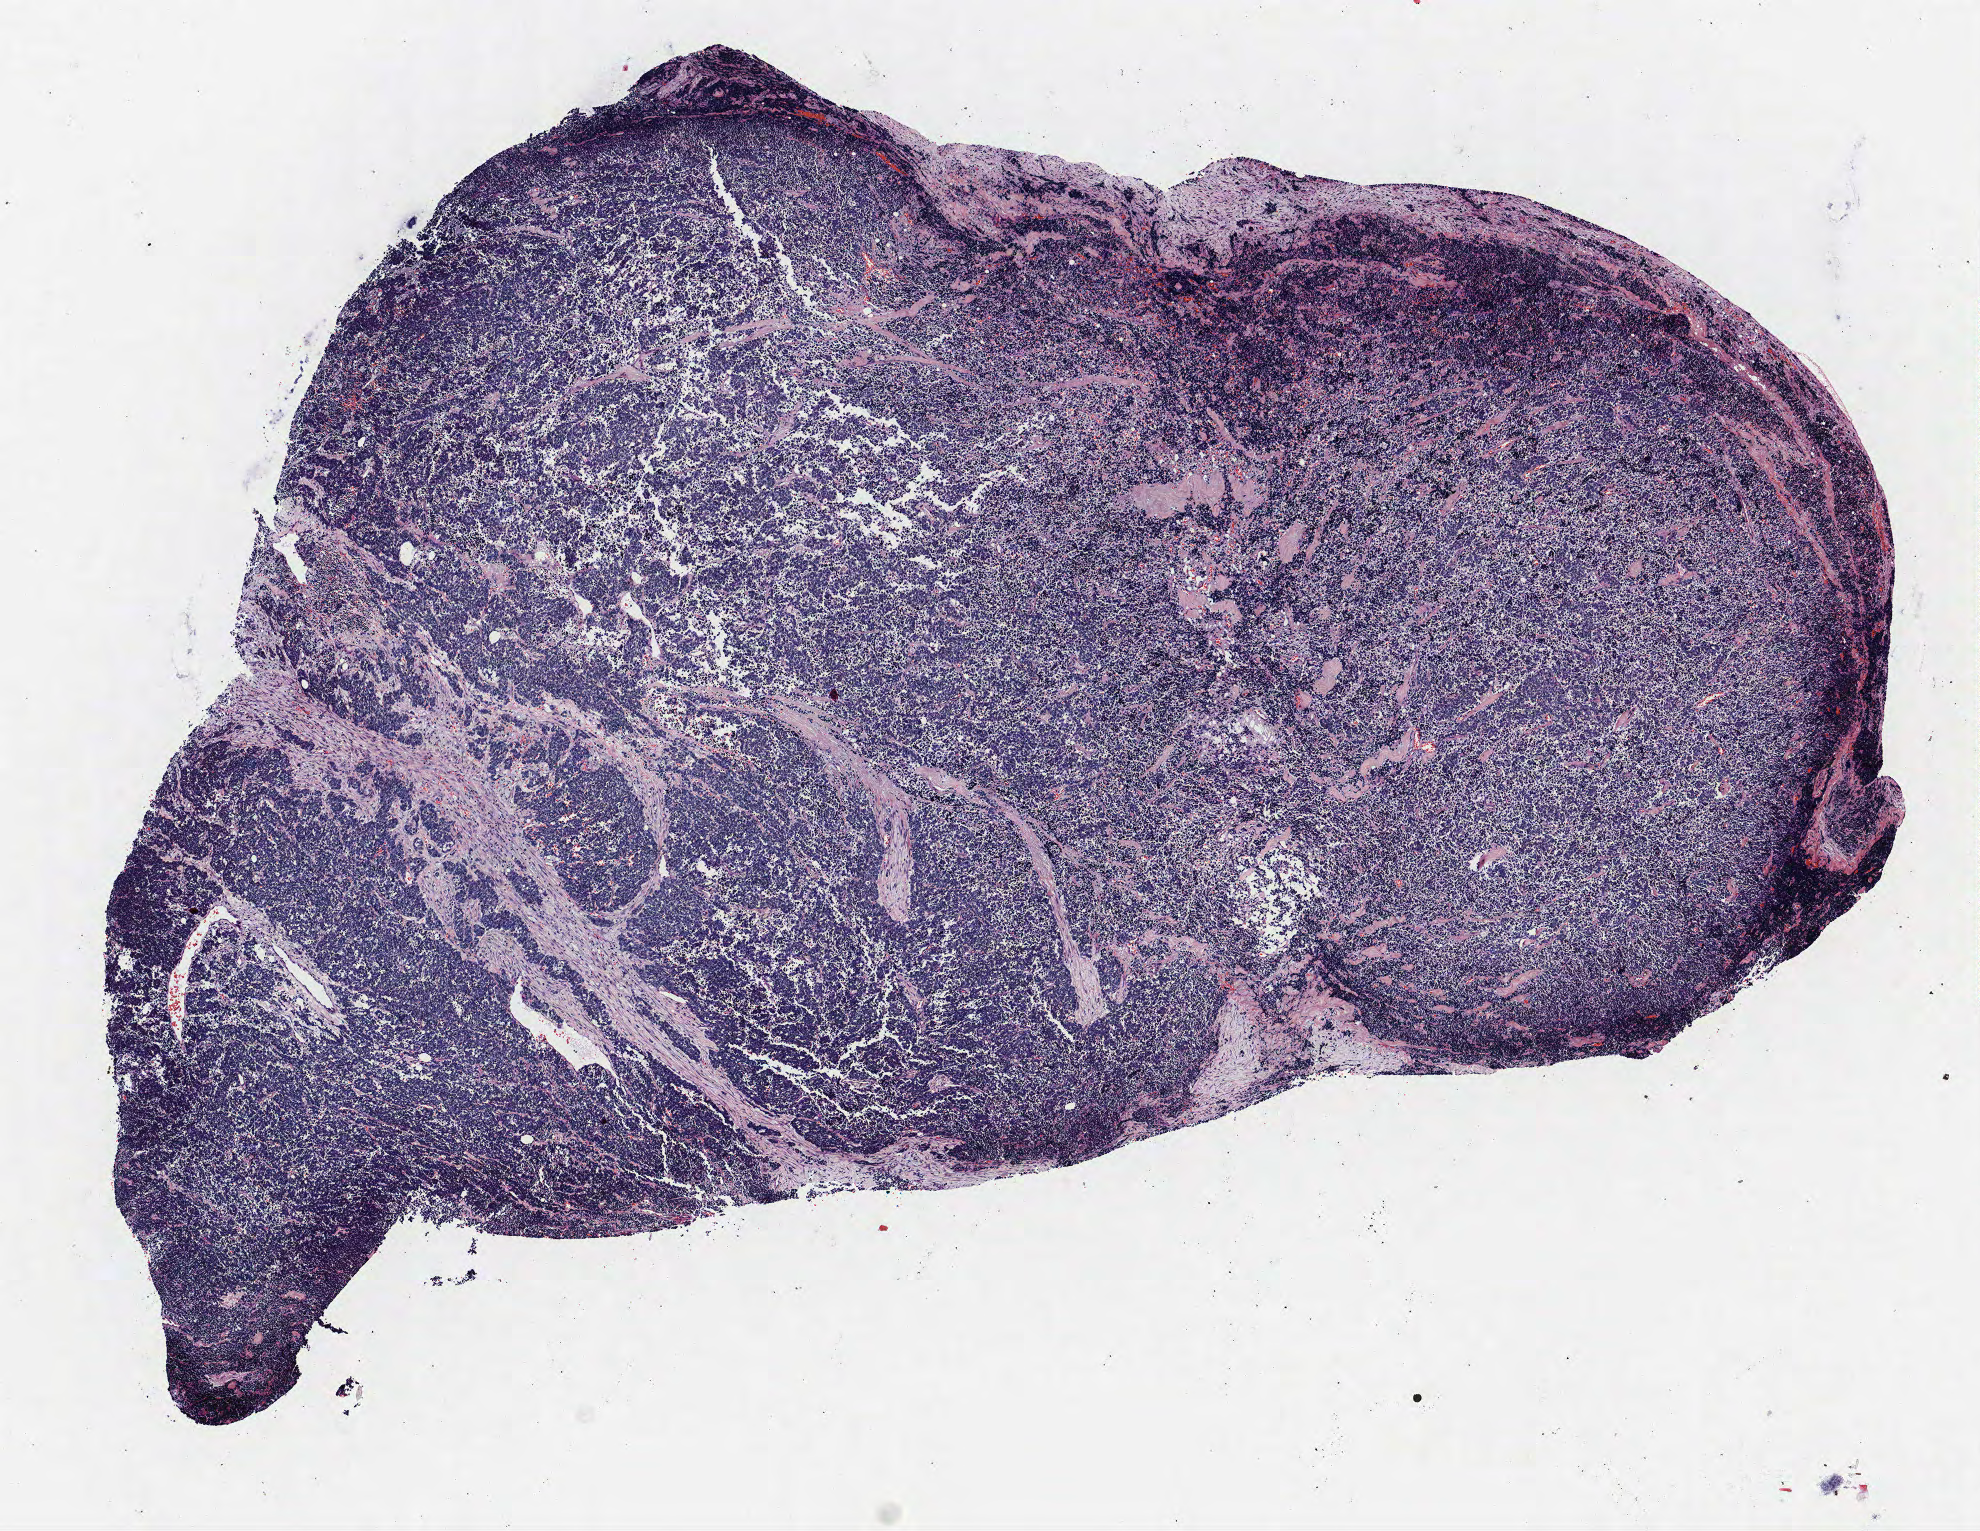
Hematoxylin and eosin (H&E) stained whole-slide image, a low-resolution overview of the entire scanned area, about 7.9 x 6.1 mm (acquisition: 40x scan). FFPE section. Lung. Male patient, aged 68 at enrolment. Current smoker at enrolment.
ICD-O-3 topography: upper lobe of lung (C34.1). Tumour size (pathology): 20 mm. Stage (AJCC 6th edition): IIIB. Participant's lung-cancer diagnosis: Small cell carcinoma, NOS. Primary tumour location (clinical record): right upper lobe.